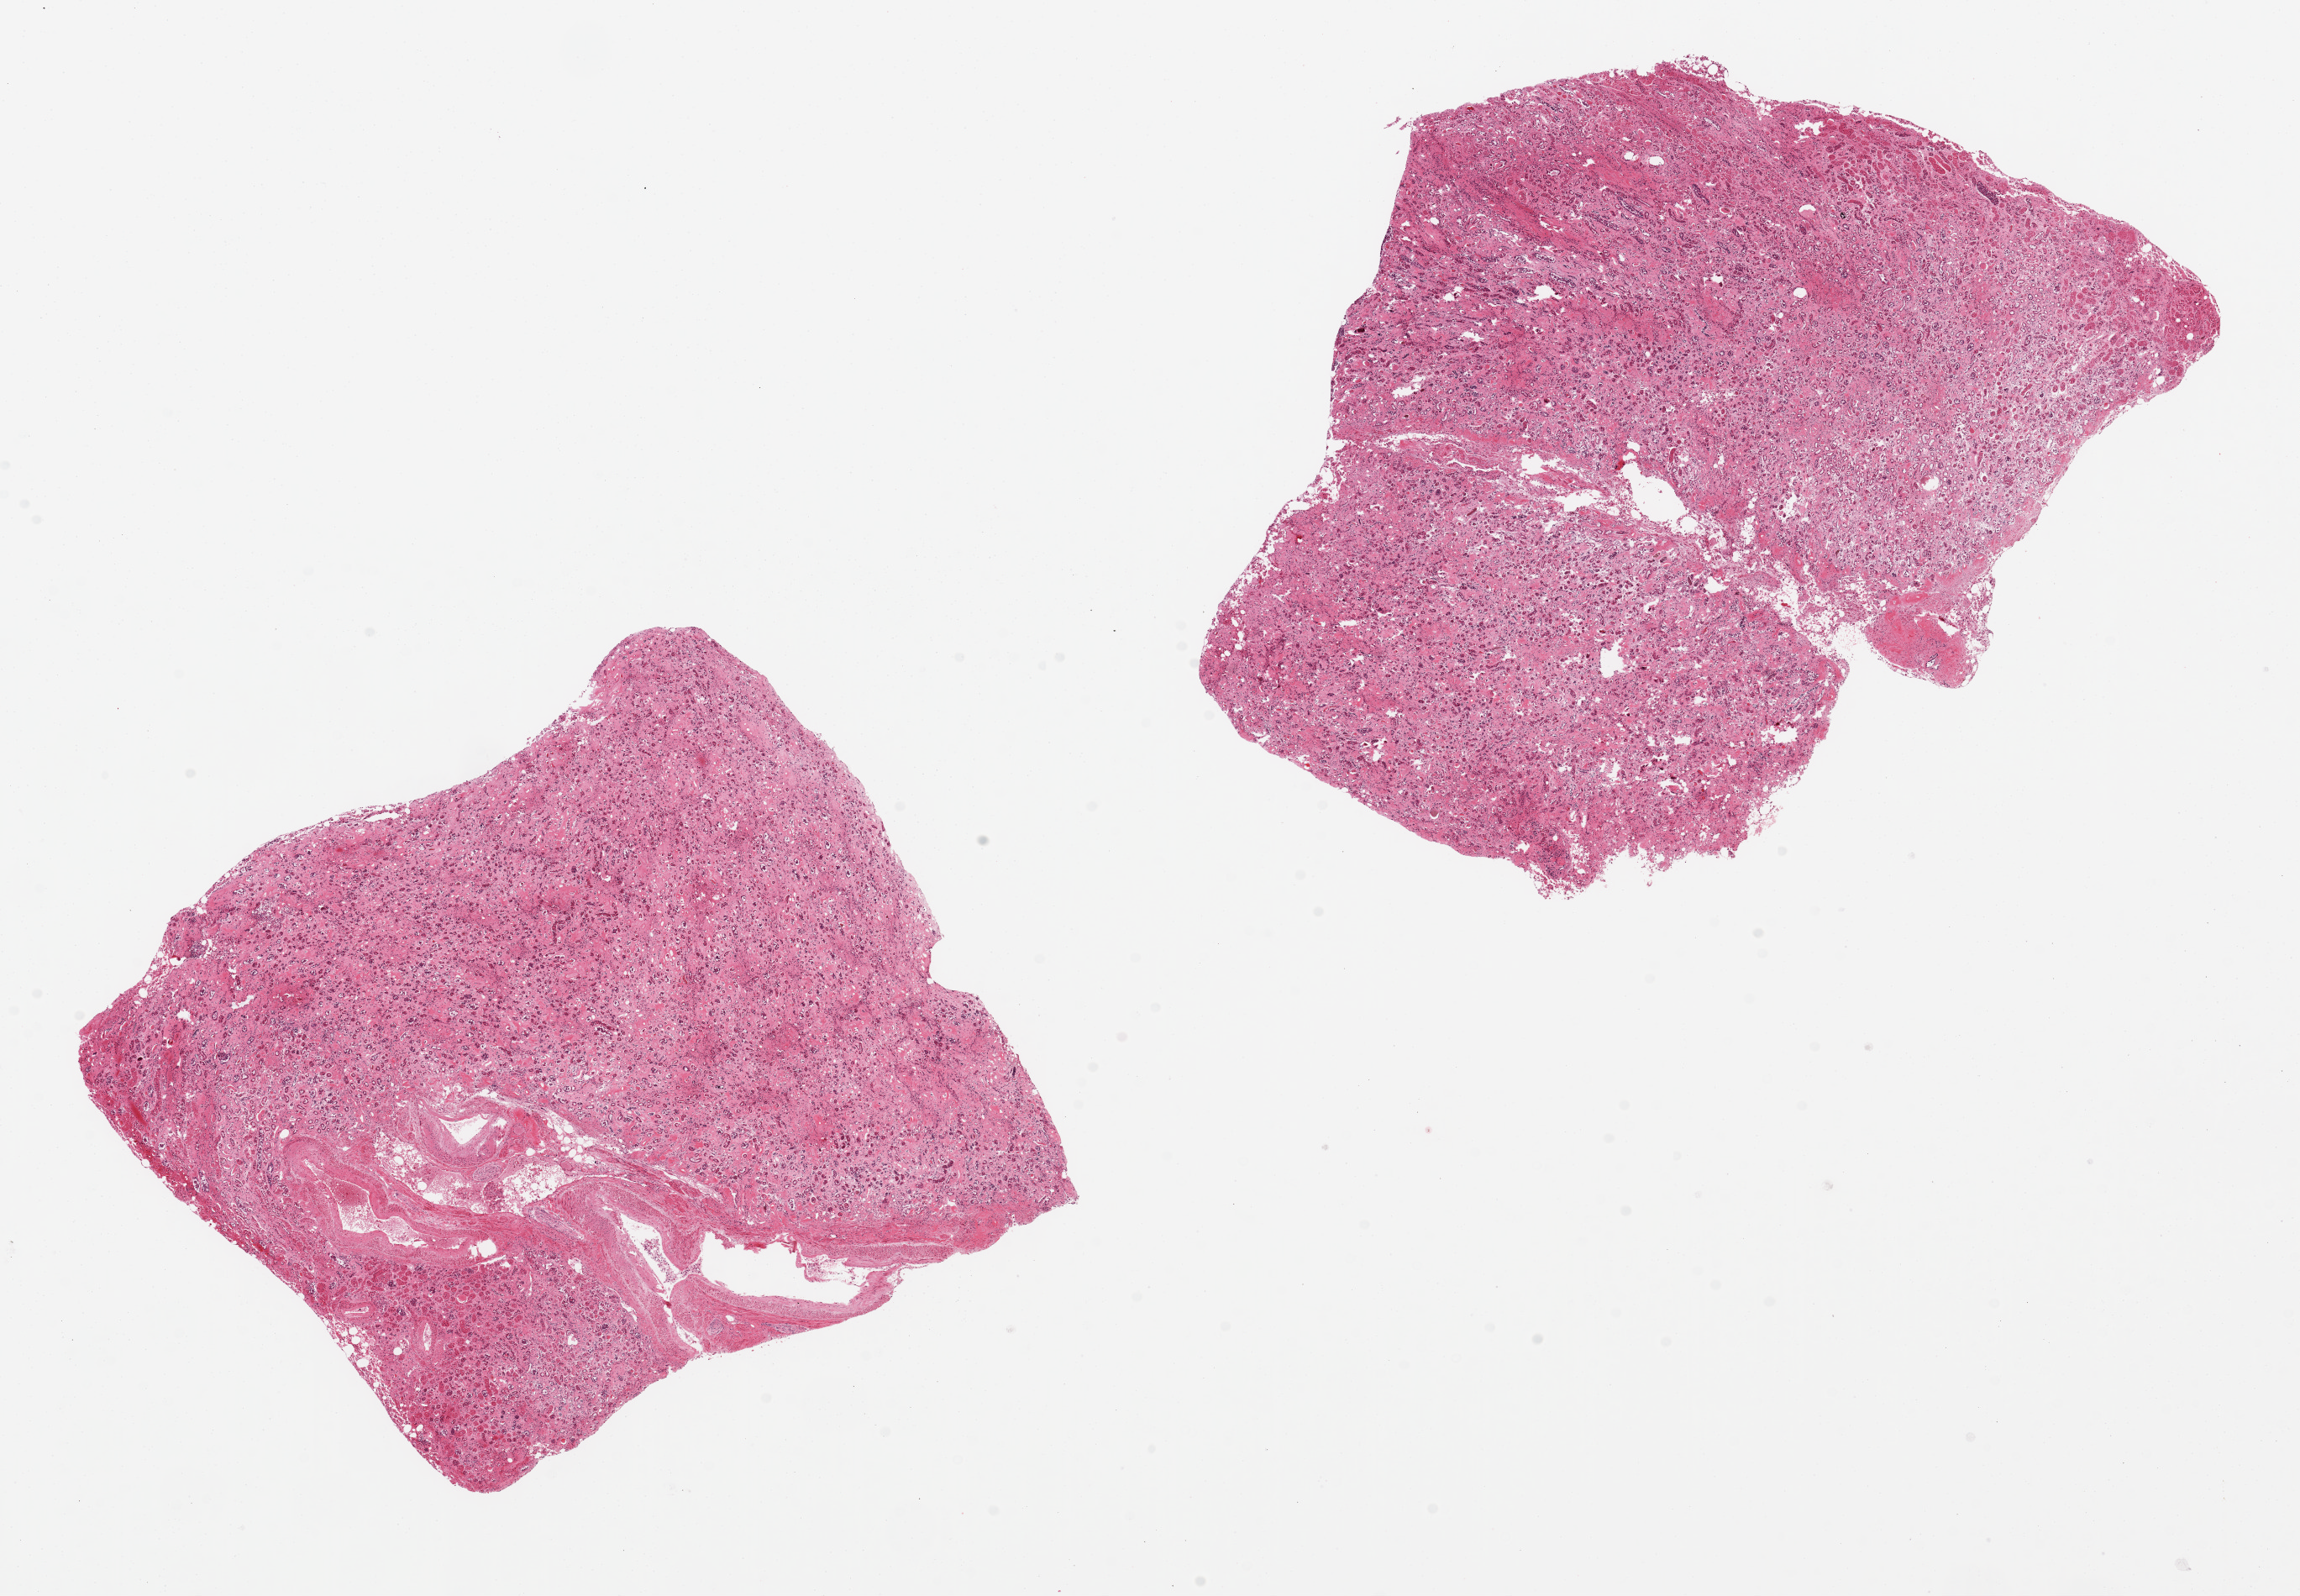
Whole-slide image, hematoxylin and eosin (H&E) stain, low-resolution overview of the scanned area, about 21.7 x 15.0 mm. PAXgene-fixed, paraffin-embedded tissue. Target tissue: renal medulla. Donor tissue sample.
• review note (as recorded): 2 aliqouts, ~7x7mm. Tubules badly autolyzed